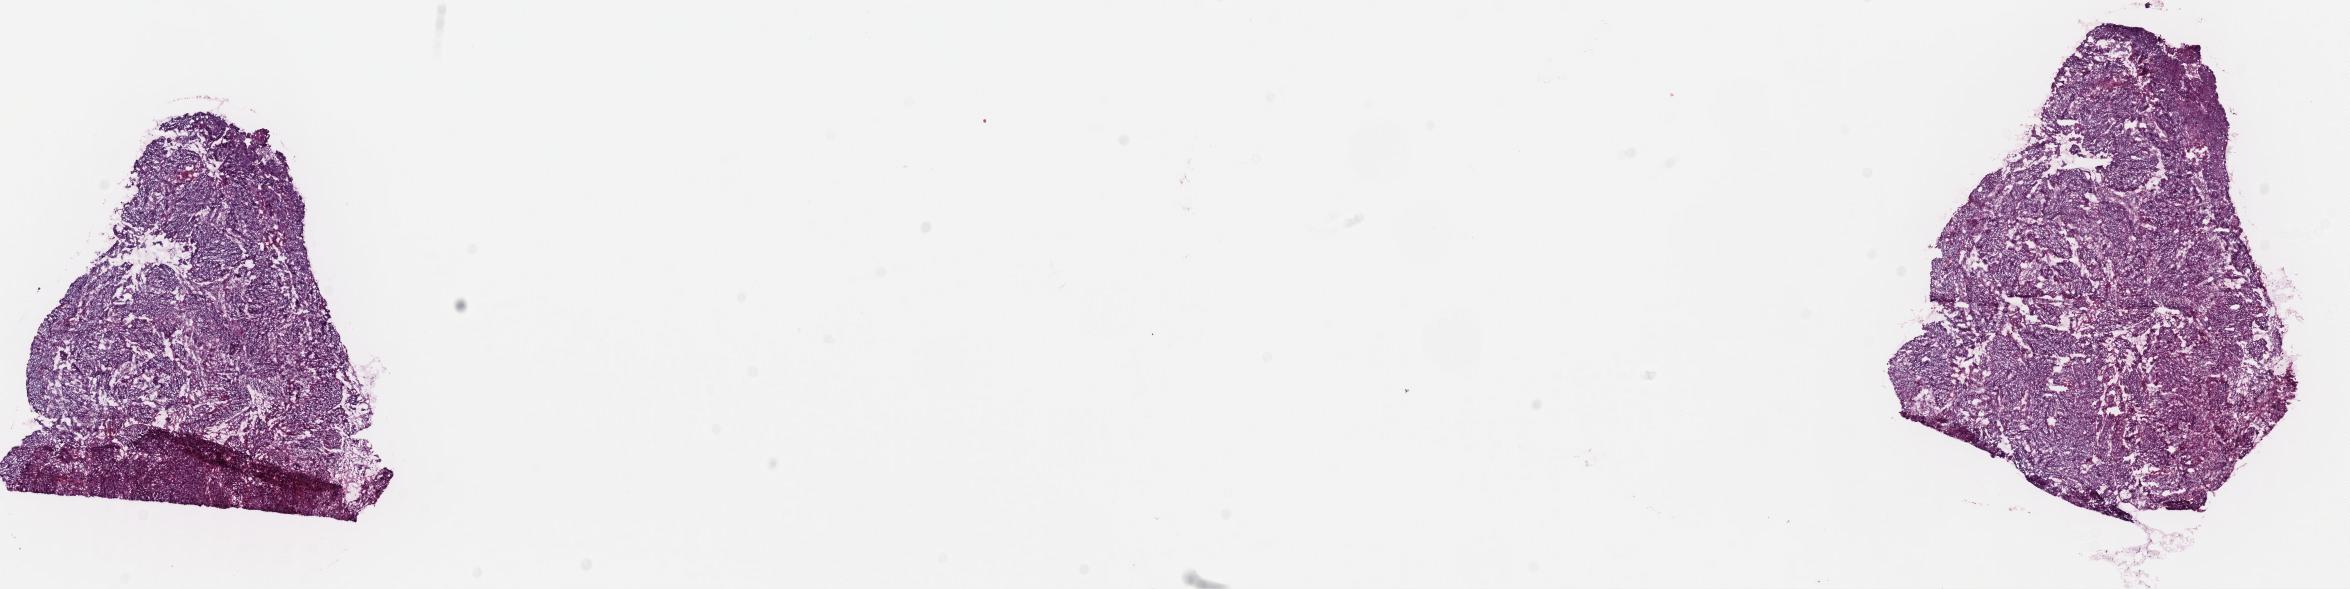
H&E-stained whole-slide image, shown as a low-resolution overview of the whole scanned area (about 18.6 x 4.7 mm, from a 40x scan), frozen section from the top of the tissue portion, sample: primary tumour, cervix. Female patient; age at initial diagnosis 48 years. Histologic grade: G3 (poorly differentiated). Slide review estimates, as recorded: tumour cells 84%, tumour nuclei 92%, normal cells 0%, stromal cells 15%, necrosis 1%. Infiltration values recorded for this section: lymphocyte infiltration 5%, monocyte infiltration 0%, neutrophil infiltration 0%.
Diagnosis: Squamous cell carcinoma, NOS (cervix uteri). FIGO stage: IVB.